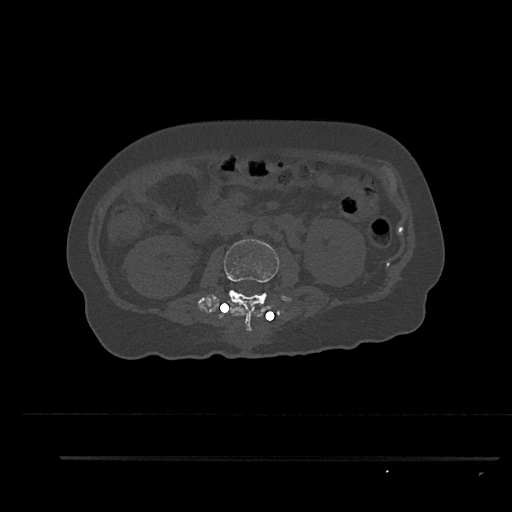
CT including the spine, one axial slice; slice 145 of 797 in the series (ordered by position); reconstruction kernel Br40s/3; 120 kVp; bone window (W 1800 / L 400 HU); 0.5 mm slice thickness; 512 × 512 image matrix, field of view 408 × 408 mm. Female patient, age 44 years. Case-level facts recorded for this patient, not image findings: primary cancer: renal; vertebrae with lytic lesions (as recorded): L1.
Annotated regions visible in this slice (semi-automatic segmentation, software-assisted and operator-edited):
- L2 vertebra: bounding box <197,239,279,331> (left, top, right, bottom; pixels)